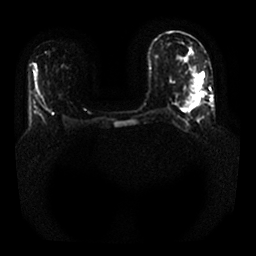
Breast MRI, one axial slice. Slice 10 of 25 in the series (ordered by position). Diffusion-weighted series; image 2 of 4 stored at this slice position (different b-values; order by instance number). 1.5 T. 256 × 256 image matrix. Female patient.
Structures marked on this image (outlined manually by an expert reader):
- tumour on diffusion-weighted imaging: box from (x=193, y=72) to (x=204, y=87) px